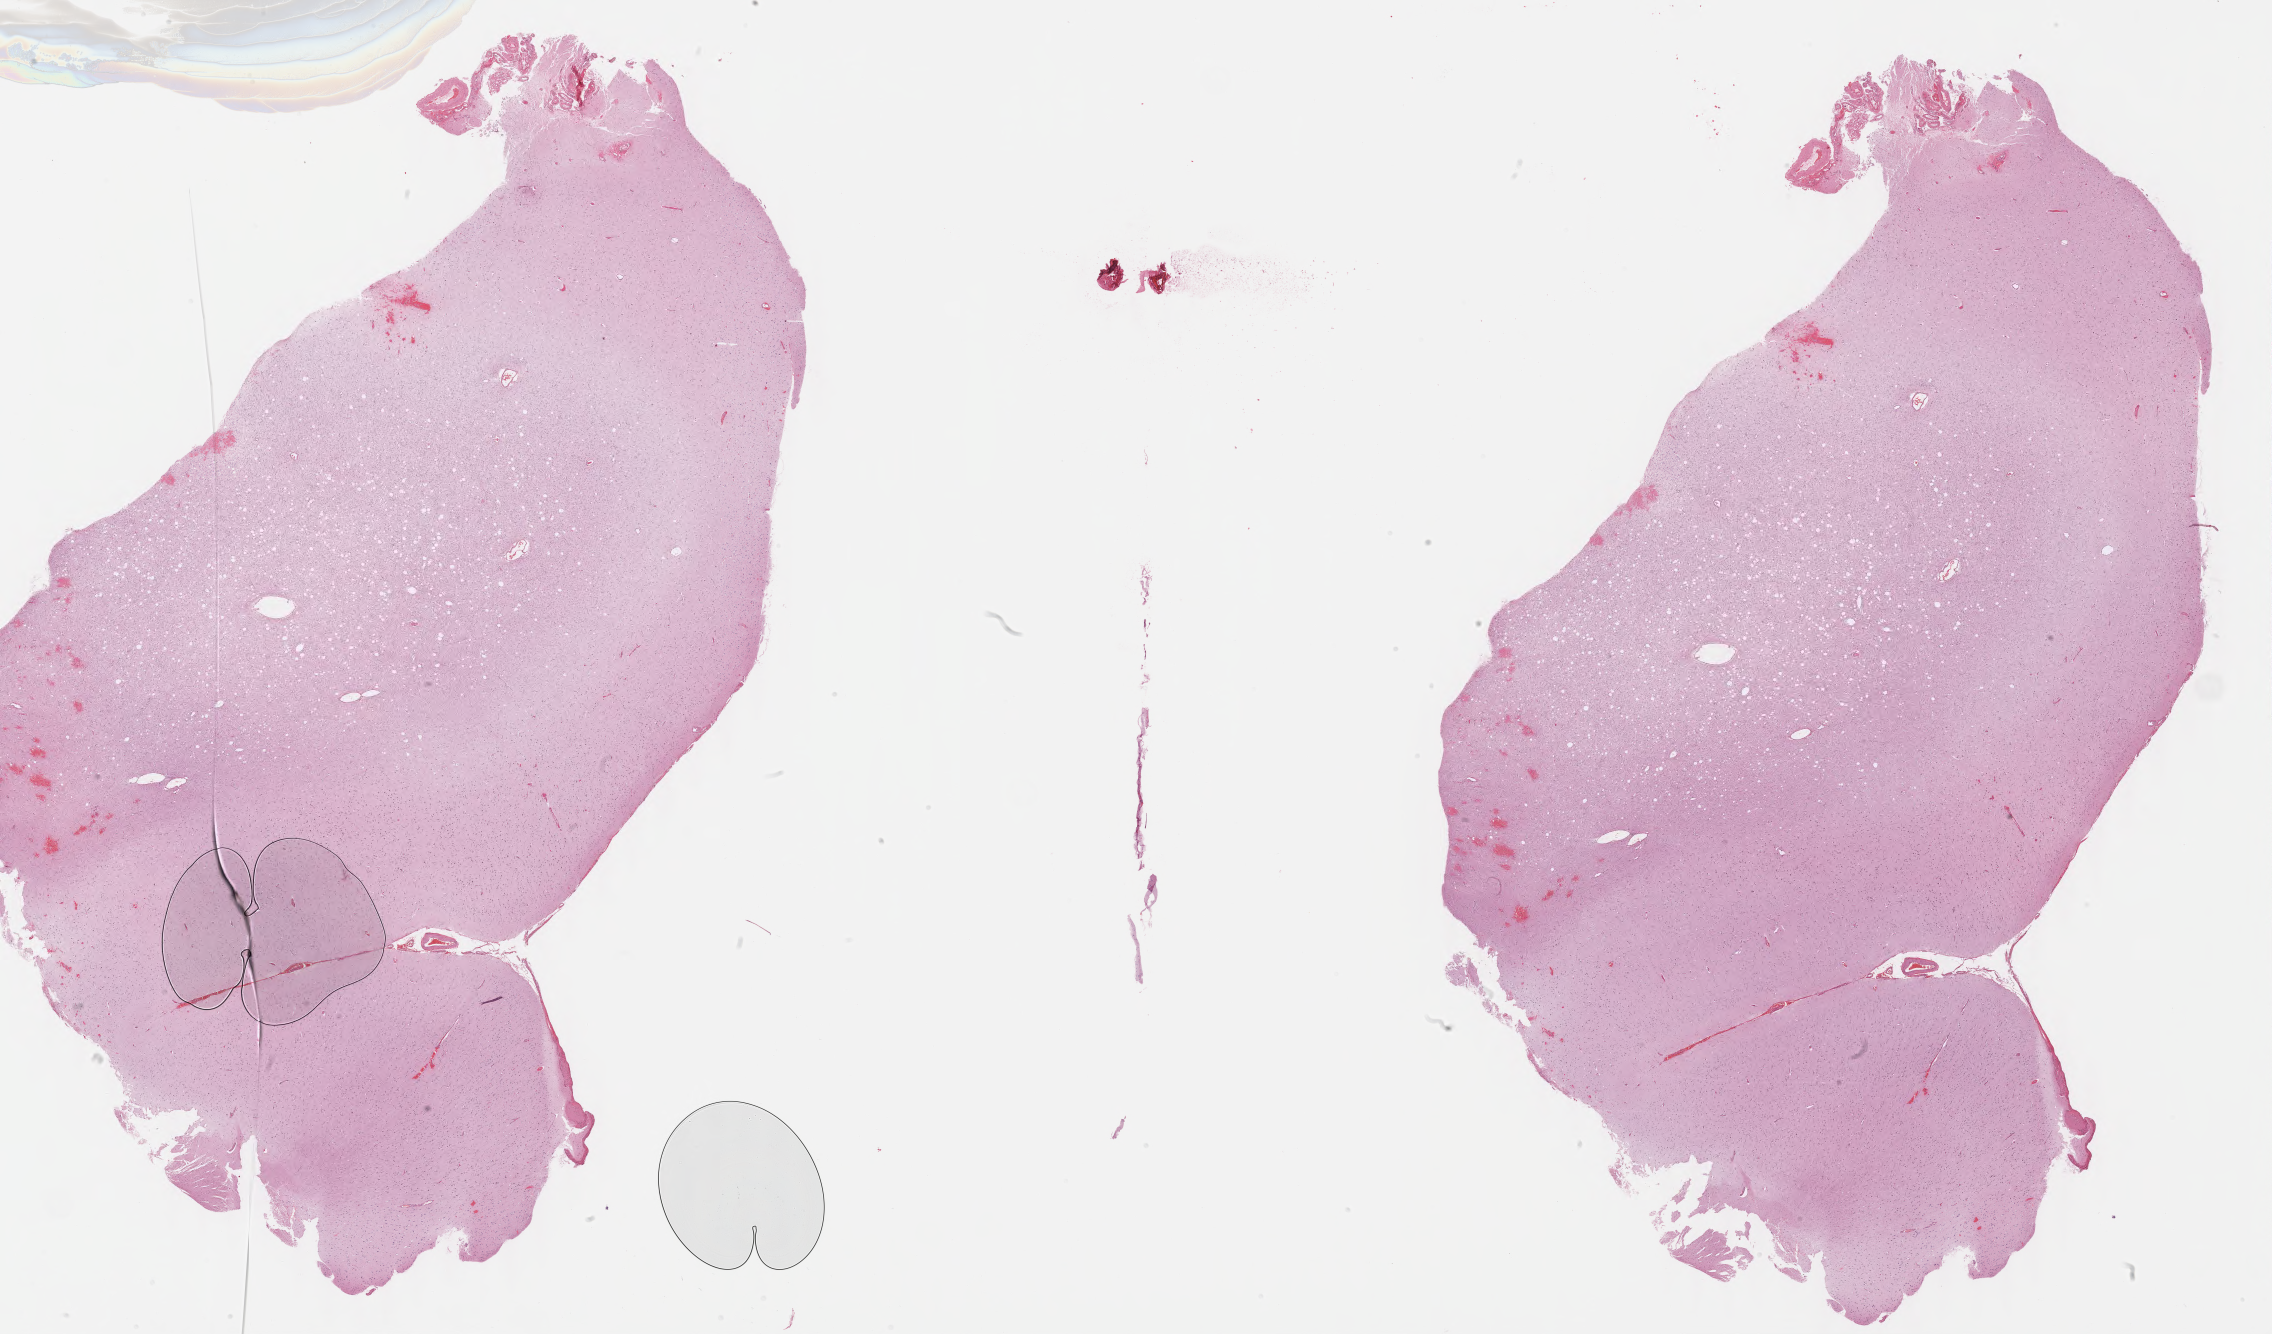
H&E-stained whole-slide image, a low-resolution overview of the entire scanned area, about 35.9 x 21.1 mm, FFPE section, brain, primary tumour sample. Male, age 20 years at initial diagnosis.
Pathologic diagnosis: Mixed glioma (cerebrum).